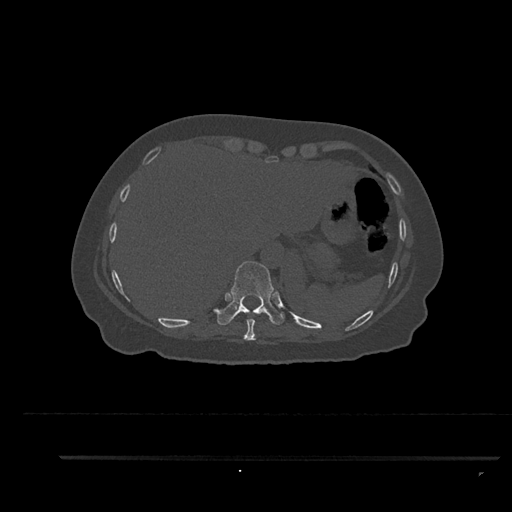
CT including the spine, one axial slice; position 378 of 797 along the scan axis; bone window (W 1800 / L 400 HU); 512 × 512 image matrix. Patient: female, 44 years. Case-level facts recorded for this patient, not image findings: primary cancer: renal.
Outlined on this slice (semi-automatic segmentation, software-assisted and operator-edited):
- T10 vertebra: bounding box [x1, y1, x2, y2] px = [215, 261, 284, 325]
- T9 vertebra: [243, 320, 256, 340]